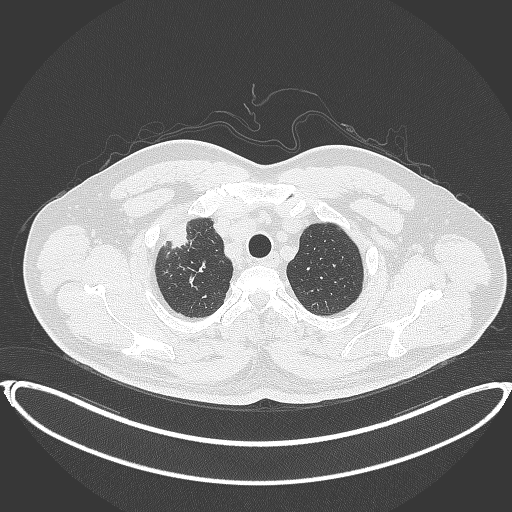
Chest CT, one axial slice; slice 340 of 399 in the series (ordered by position); 120 kVp; lung window (W 1500 / L -600 HU); 1 mm slice thickness; 512 × 512 image matrix, field of view 445 × 445 mm. Patient: male, 53 years. From the clinical record (not read from this slice): clinical TNM (as recorded): T2a N0 M0.
Annotated regions visible in this slice (rectangle marked by the reading radiologist):
- lung tumour (recorded histology: adenocarcinoma): box from (x=165, y=214) to (x=195, y=253) px